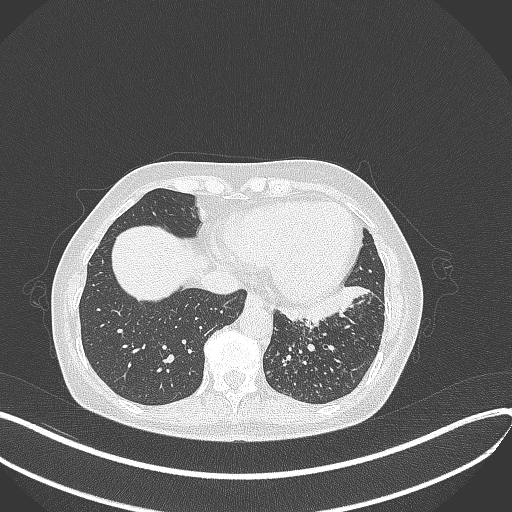
Chest CT, one axial slice; position 113 of 429 along the scan axis; lung window (W 1500 / L -600 HU); 1 mm slice thickness; 512 × 512 image matrix, field of view 400 × 400 mm. Patient: female, 63 years. Case-level facts recorded for this patient, not image findings: clinical TNM (as recorded): T1b N0 M0.
Annotated regions visible in this slice (rectangle marked by the reading radiologist):
- lung tumour (recorded histology: adenocarcinoma): bounding box [x1, y1, x2, y2] px = [282, 283, 371, 324]